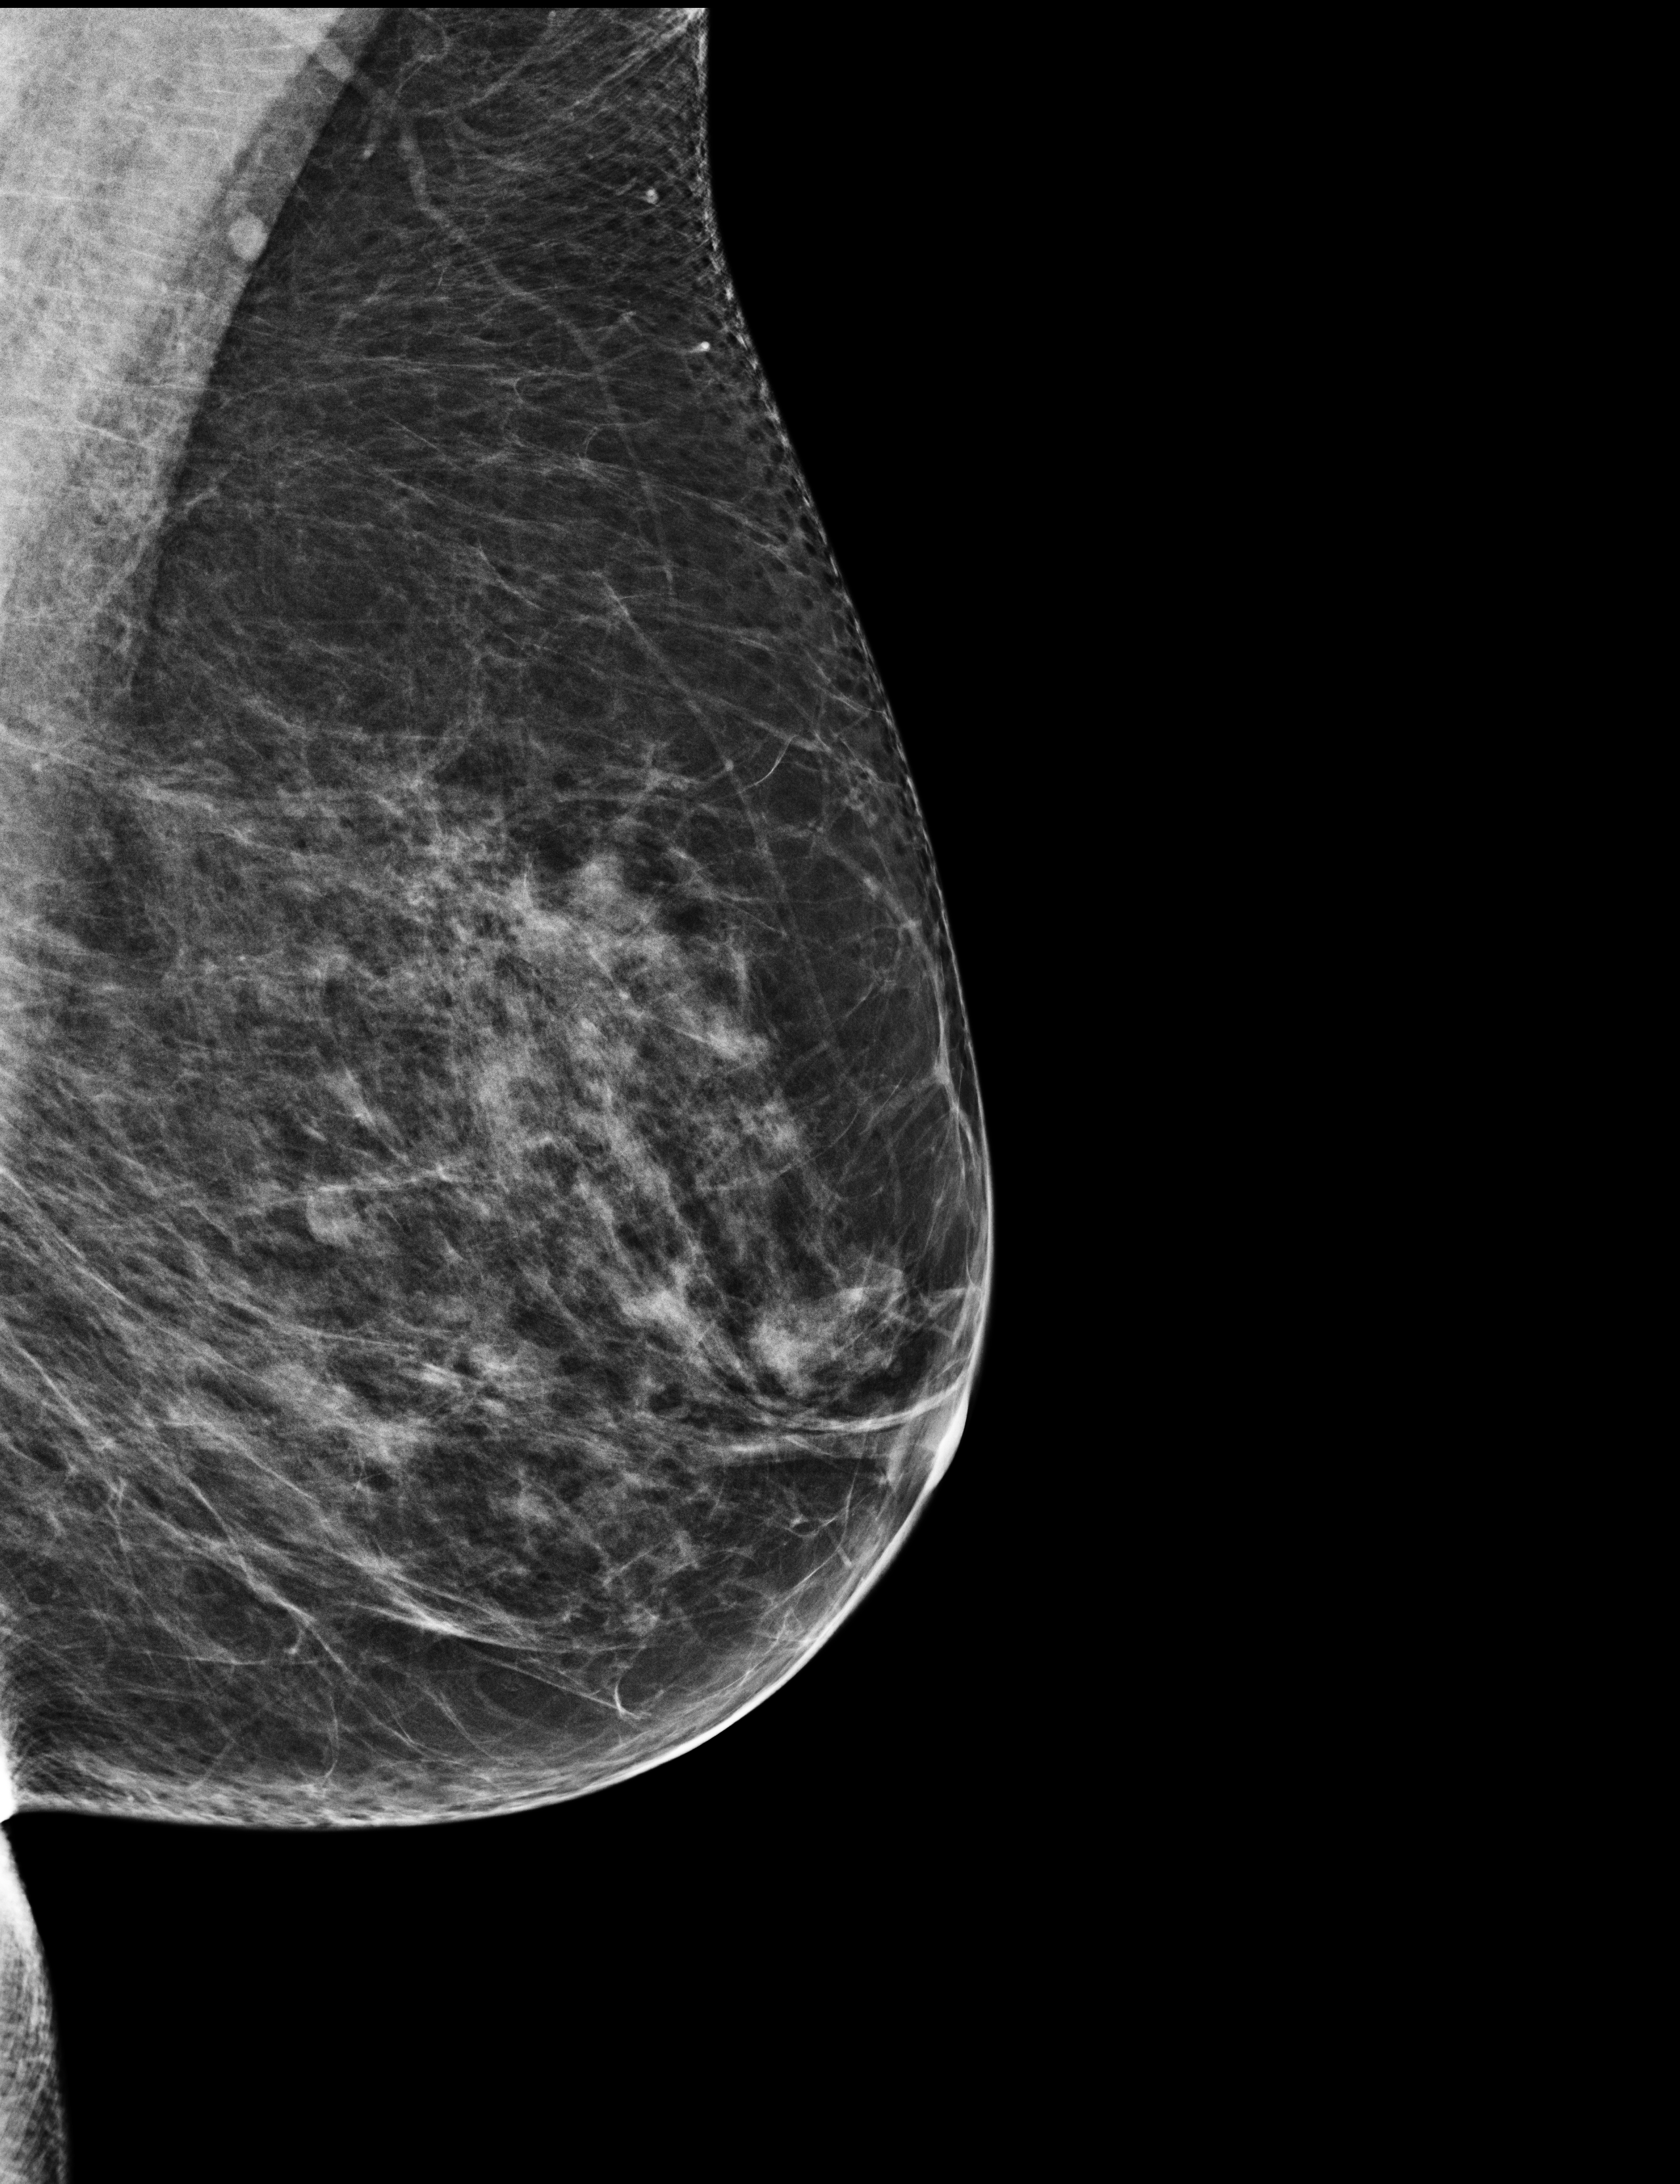
Digital mammogram (FFDM); left breast; medio-lateral oblique projection; annual screening mammography examination; compressed breast thickness 55 mm. Female patient, age 67 years.
- BI-RADS breast density category at the screening exam (both breasts, scale 1–4): 3
- final BI-RADS assessment for this screening round (tomosynthesis exam, both breasts): category 2
- recall: no recall after this screen